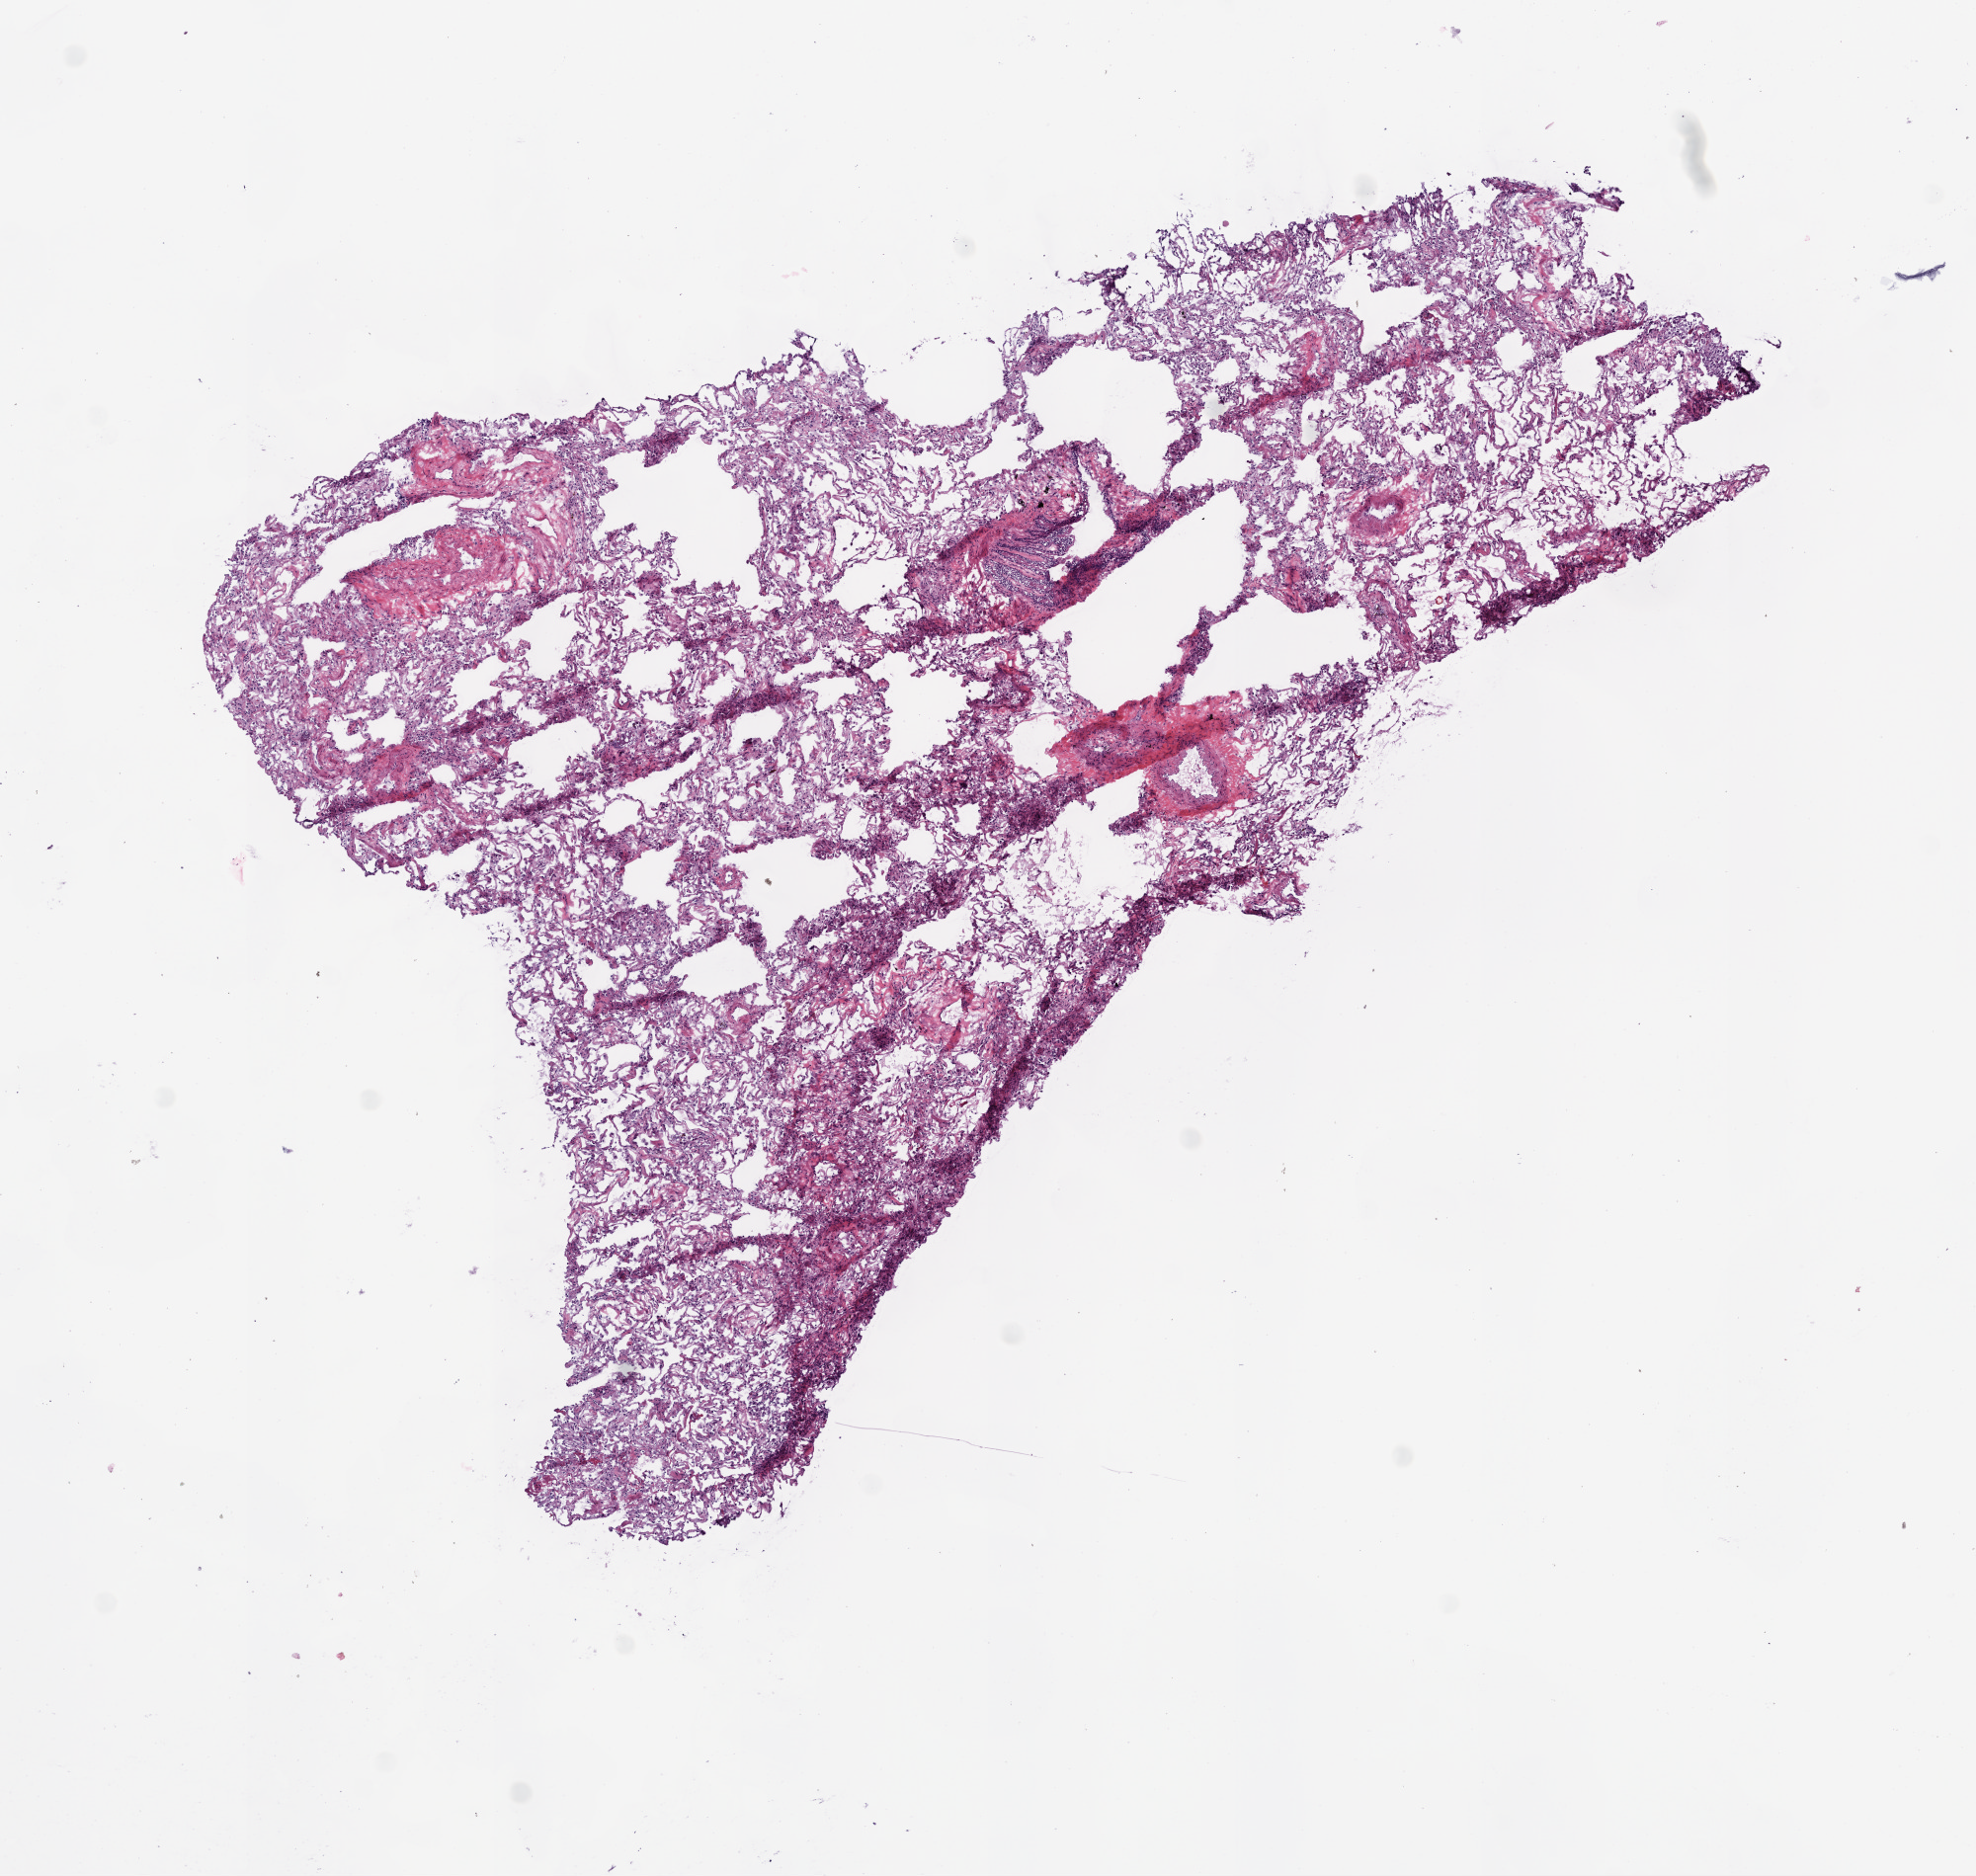
Whole-slide histology image, H&E, shown as a low-resolution overview of the whole scanned area (about 8.0 x 7.6 mm, slide scanned at 20x), frozen section from the bottom of the tissue portion, solid tissue normal (non-tumour tissue) sample from the lung. Male, age 83 years at initial diagnosis.
This section: solid tissue normal sample (biorepository sample class). Patient diagnosis: Squamous cell carcinoma, NOS (upper lobe, lung).